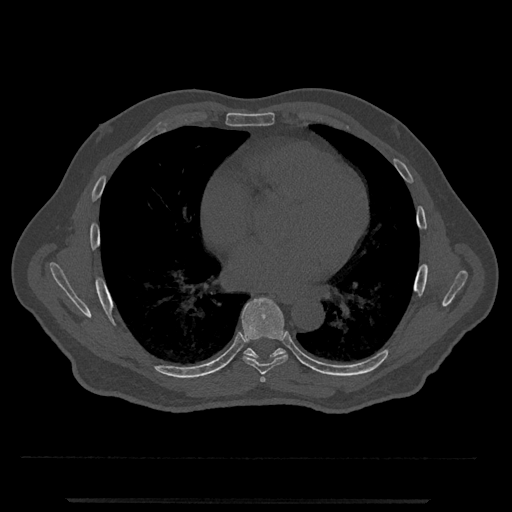
CT including the spine, one axial slice; position 665 of 797 along the scan axis; 120 kVp; bone window (W 1800 / L 400 HU); 0.5 mm slice thickness; 512 × 512 image matrix, field of view 419 × 419 mm. Patient: male, 63 years. Case-level facts recorded for this patient, not image findings: primary cancer: prostate.
Structures marked on this image (semi-automatically segmented with operator editing):
- T6 vertebra: bounding box <260,376,266,383> (left, top, right, bottom; pixels)
- T7 vertebra: <241,297,288,374>
- T8 vertebra: <244,348,286,359>